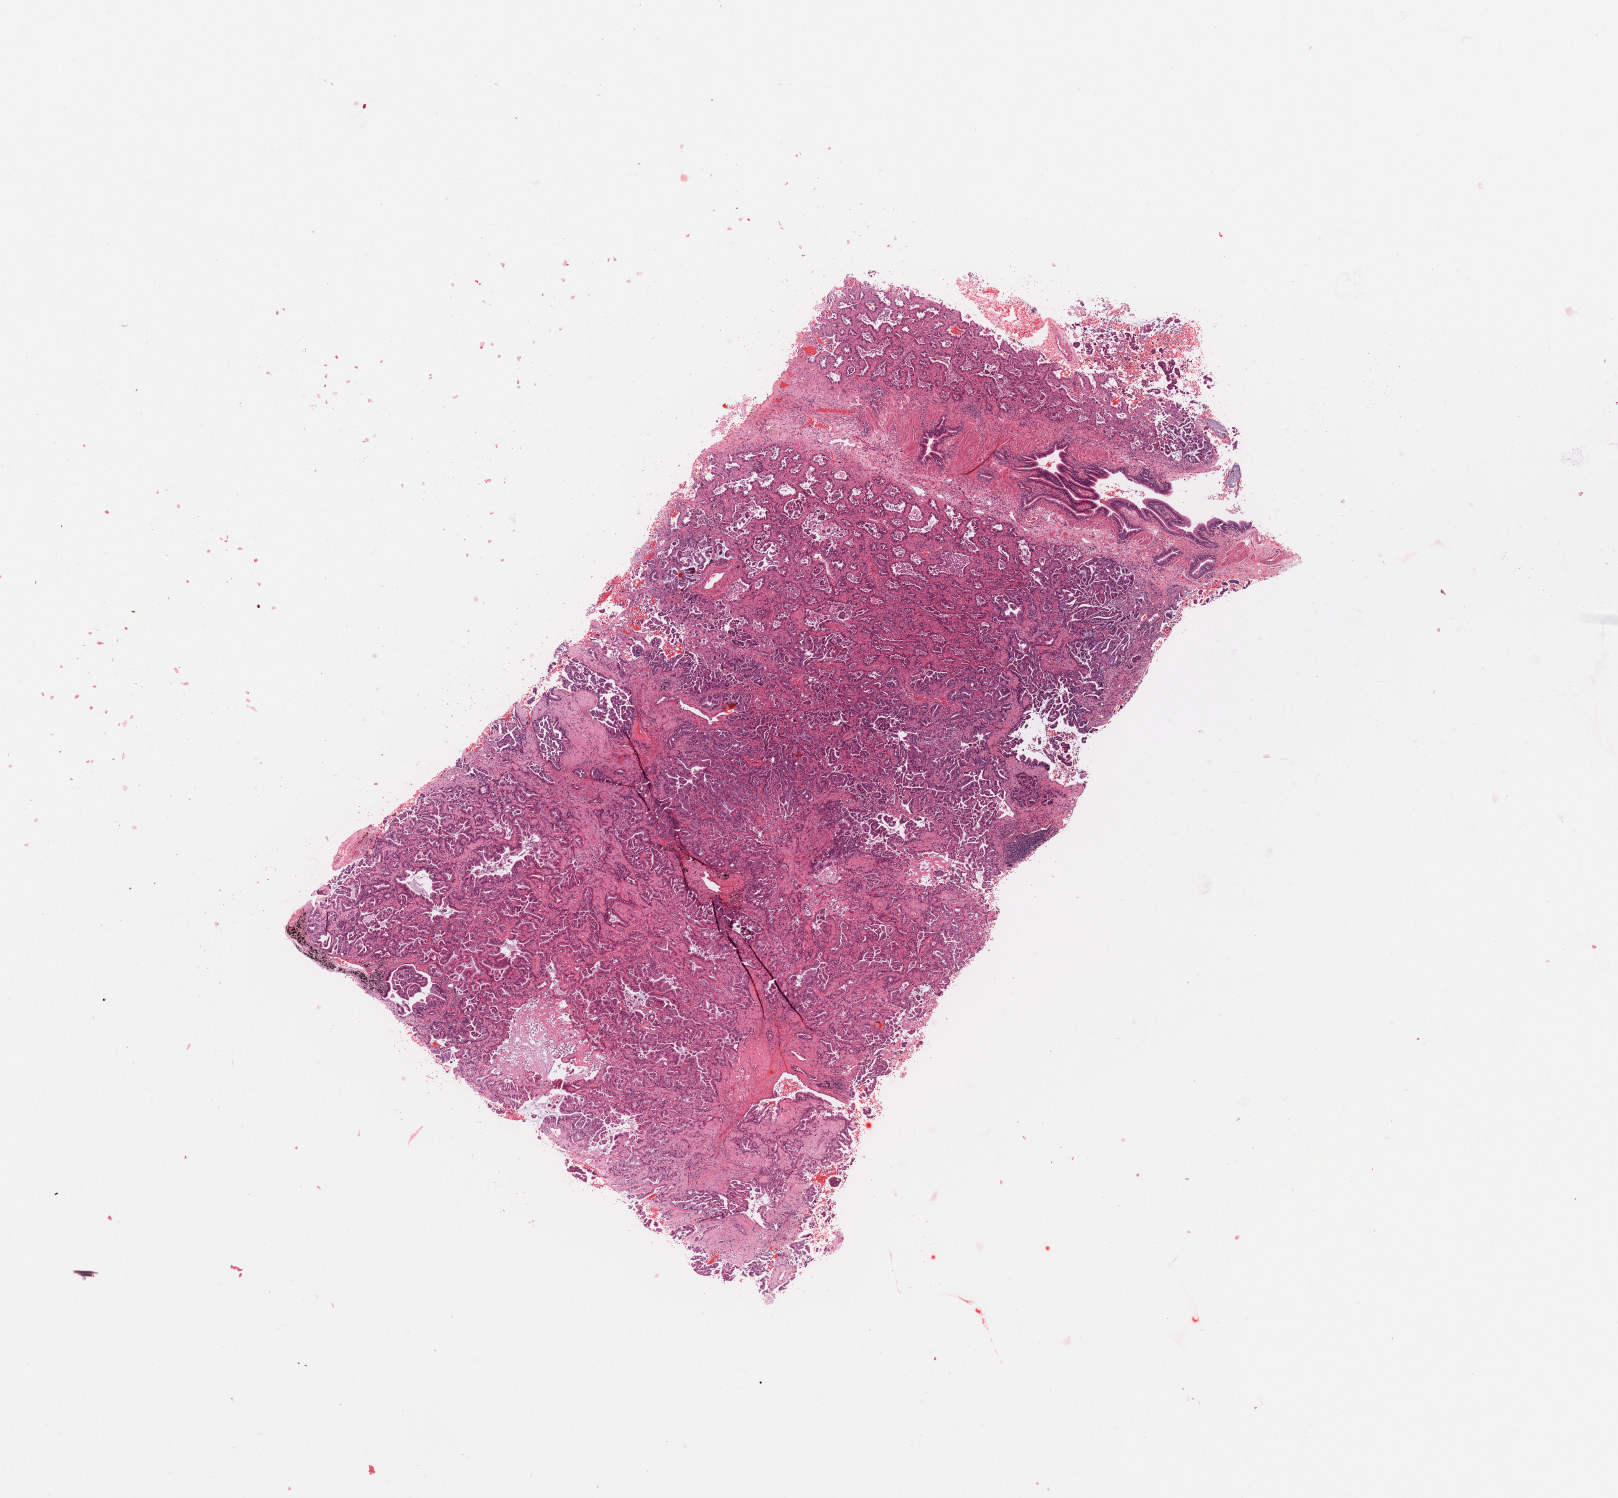
Digitized H&E tissue section (whole slide) — a low-resolution overview of the entire scanned area, about 12.8 x 11.8 mm (slide scanned at 20x), tumour tissue sample, sampled site: lung. Patient: female, age 56 years. Histologic grade: G3 (poorly differentiated). Slide review estimates, as recorded: tumour nuclei 80%, necrosis 2%.
• primary tumour site (as recorded): right upper lobe
• AJCC pathologic stage: IV
• diagnosis: Adenocarcinoma, NOS